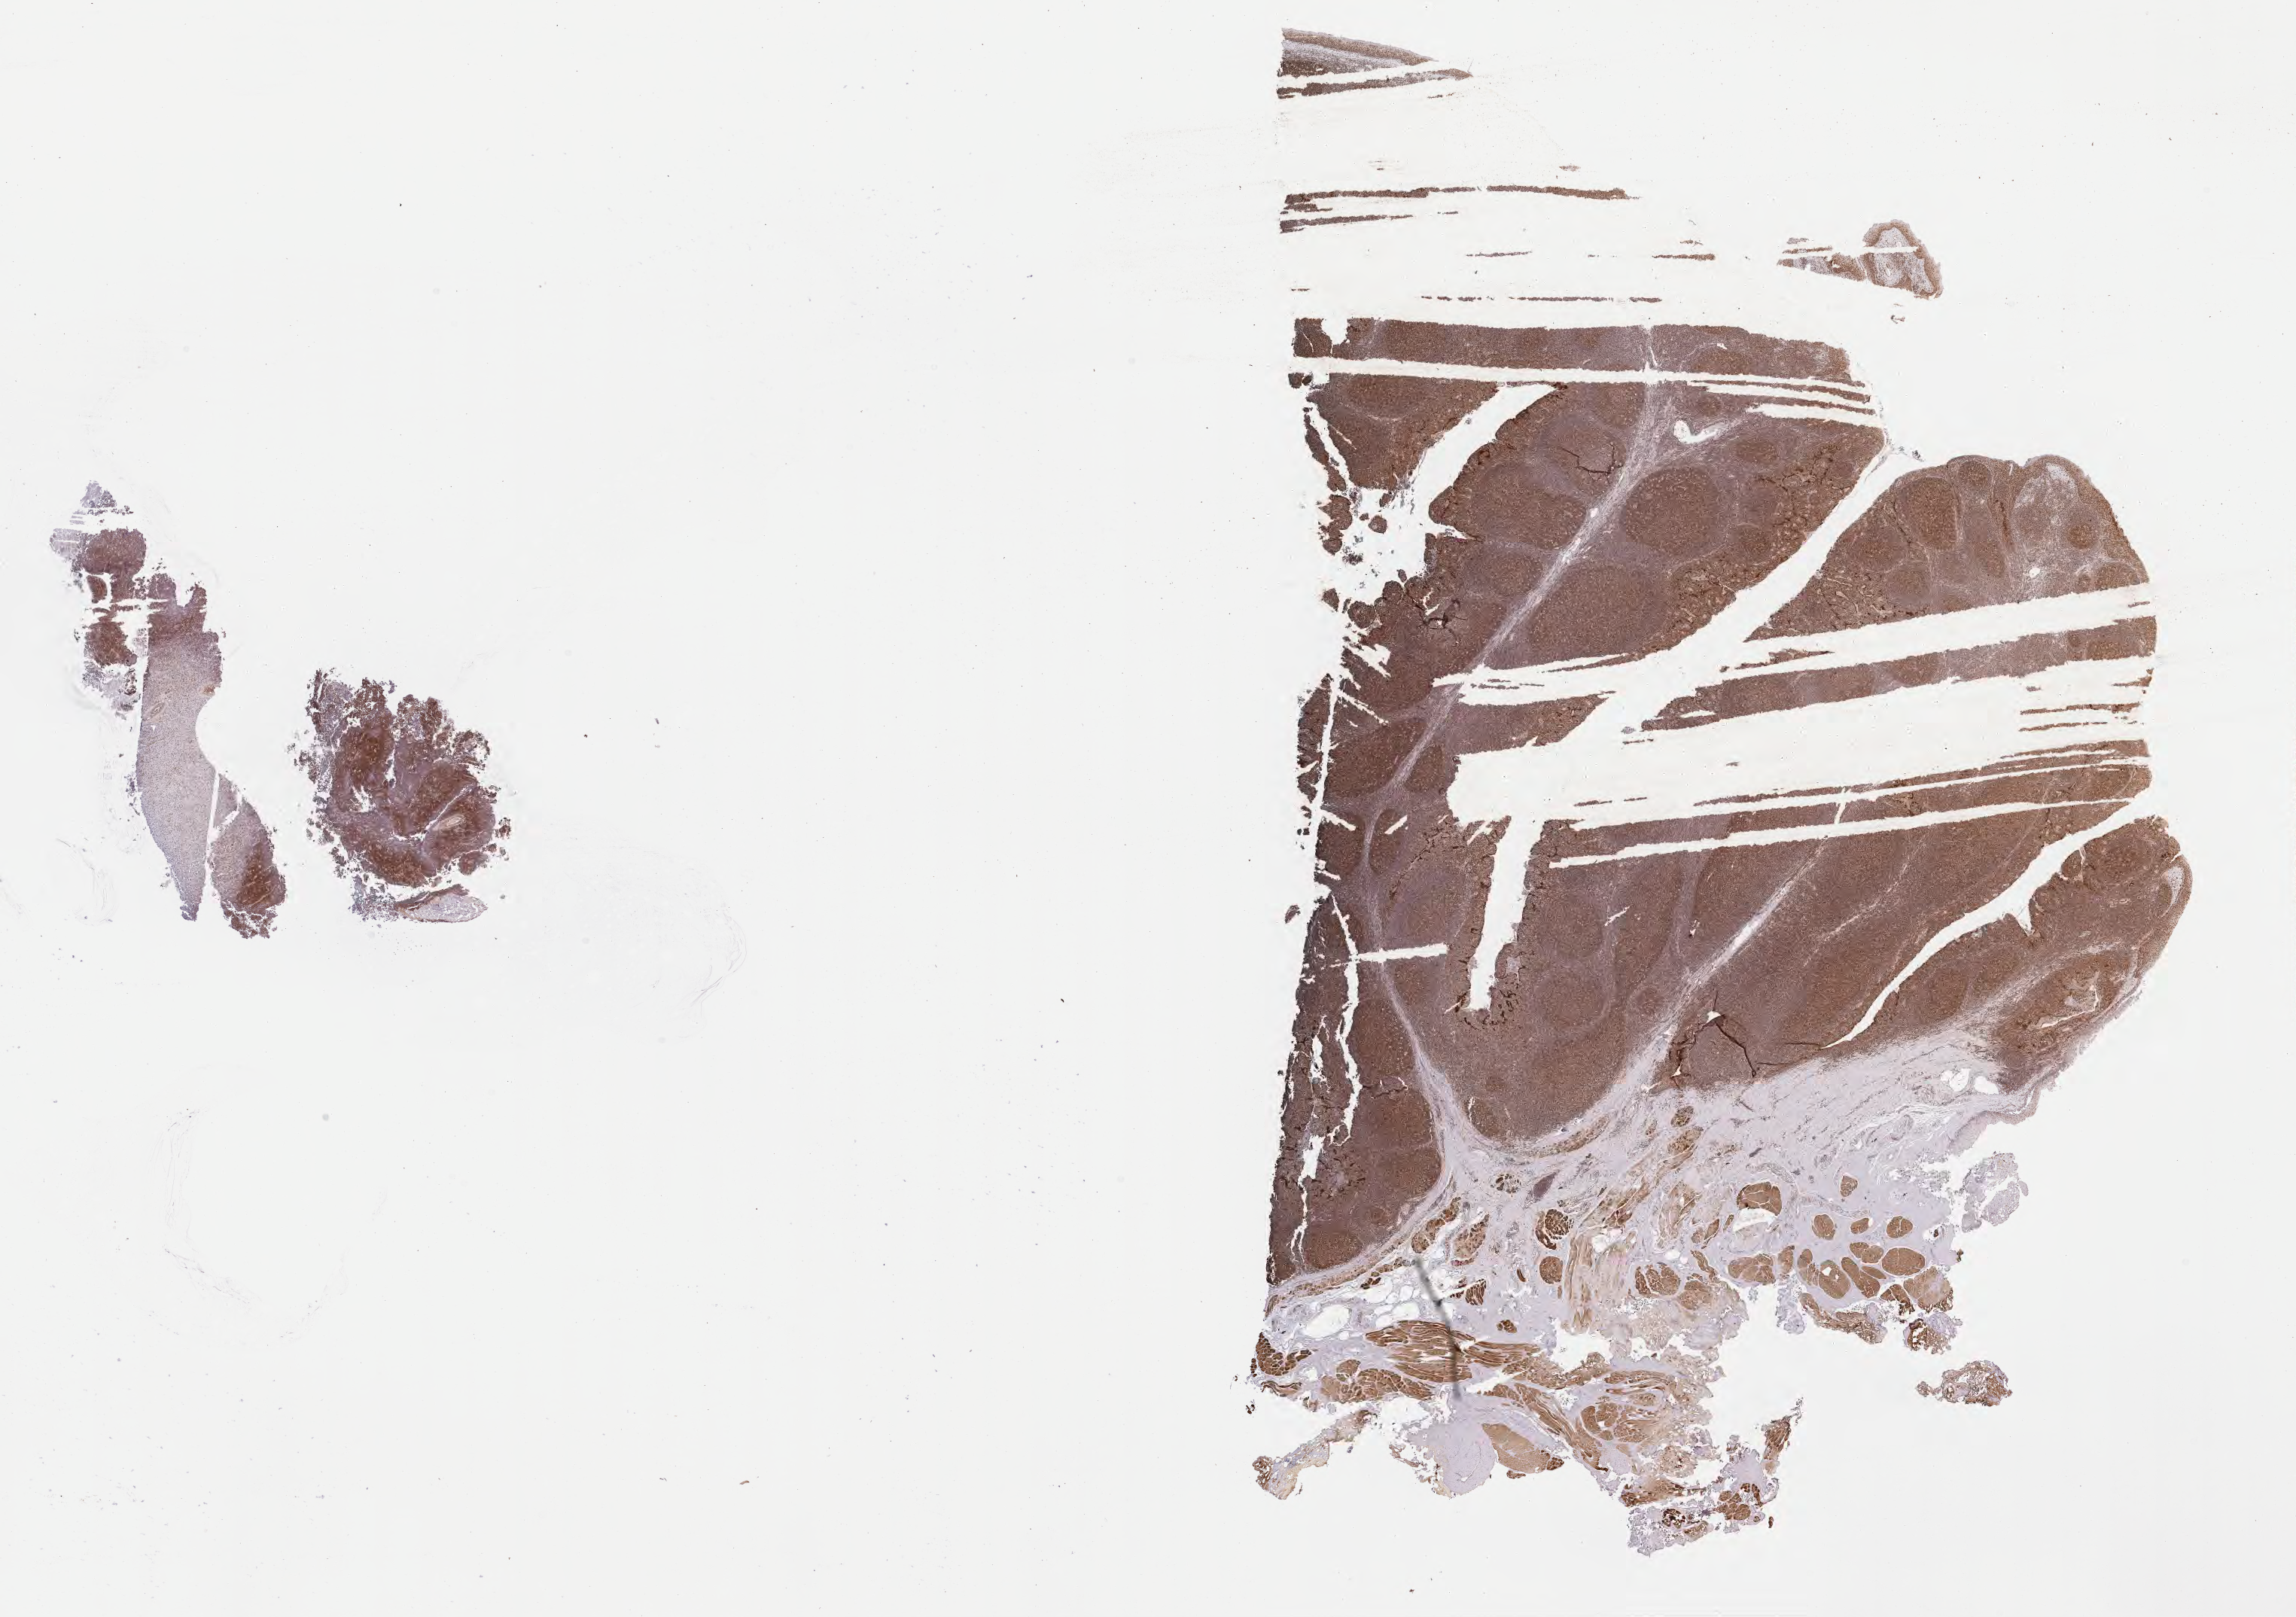
Whole-slide image, immunohistochemical stain for BCL6, low-resolution overview of the scanned area, about 24.7 x 17.4 mm. Specimen: tumor tissue. Site: cranium. Male, age 4 years at initial diagnosis.
Histologic diagnosis: Burkitt lymphoma, NOS.